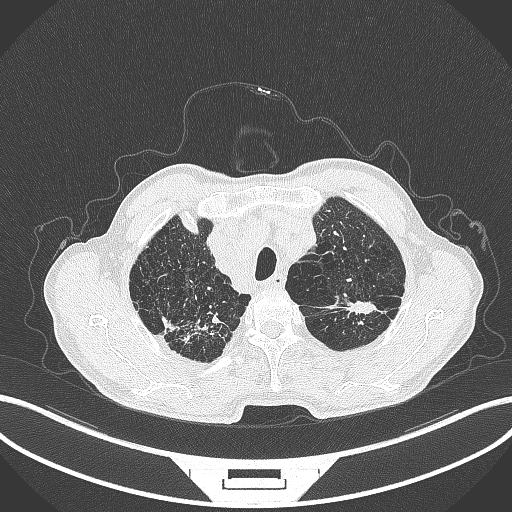
Chest CT, one axial slice. Position 379 of 463 along the scan axis. Reconstruction kernel B70f. 120 kVp. Lung window (W 1500 / L -600 HU). 512 × 512 image matrix, field of view 400 × 400 mm. Patient: male, 74 years. Case-level facts recorded for this patient, not image findings: clinical TNM (as recorded): T2a N1 M0.
Outlined on this slice (rectangle marked by the reading radiologist):
- lung tumour (recorded histology: adenocarcinoma): bounding box [x1, y1, x2, y2] px = [339, 296, 380, 320]